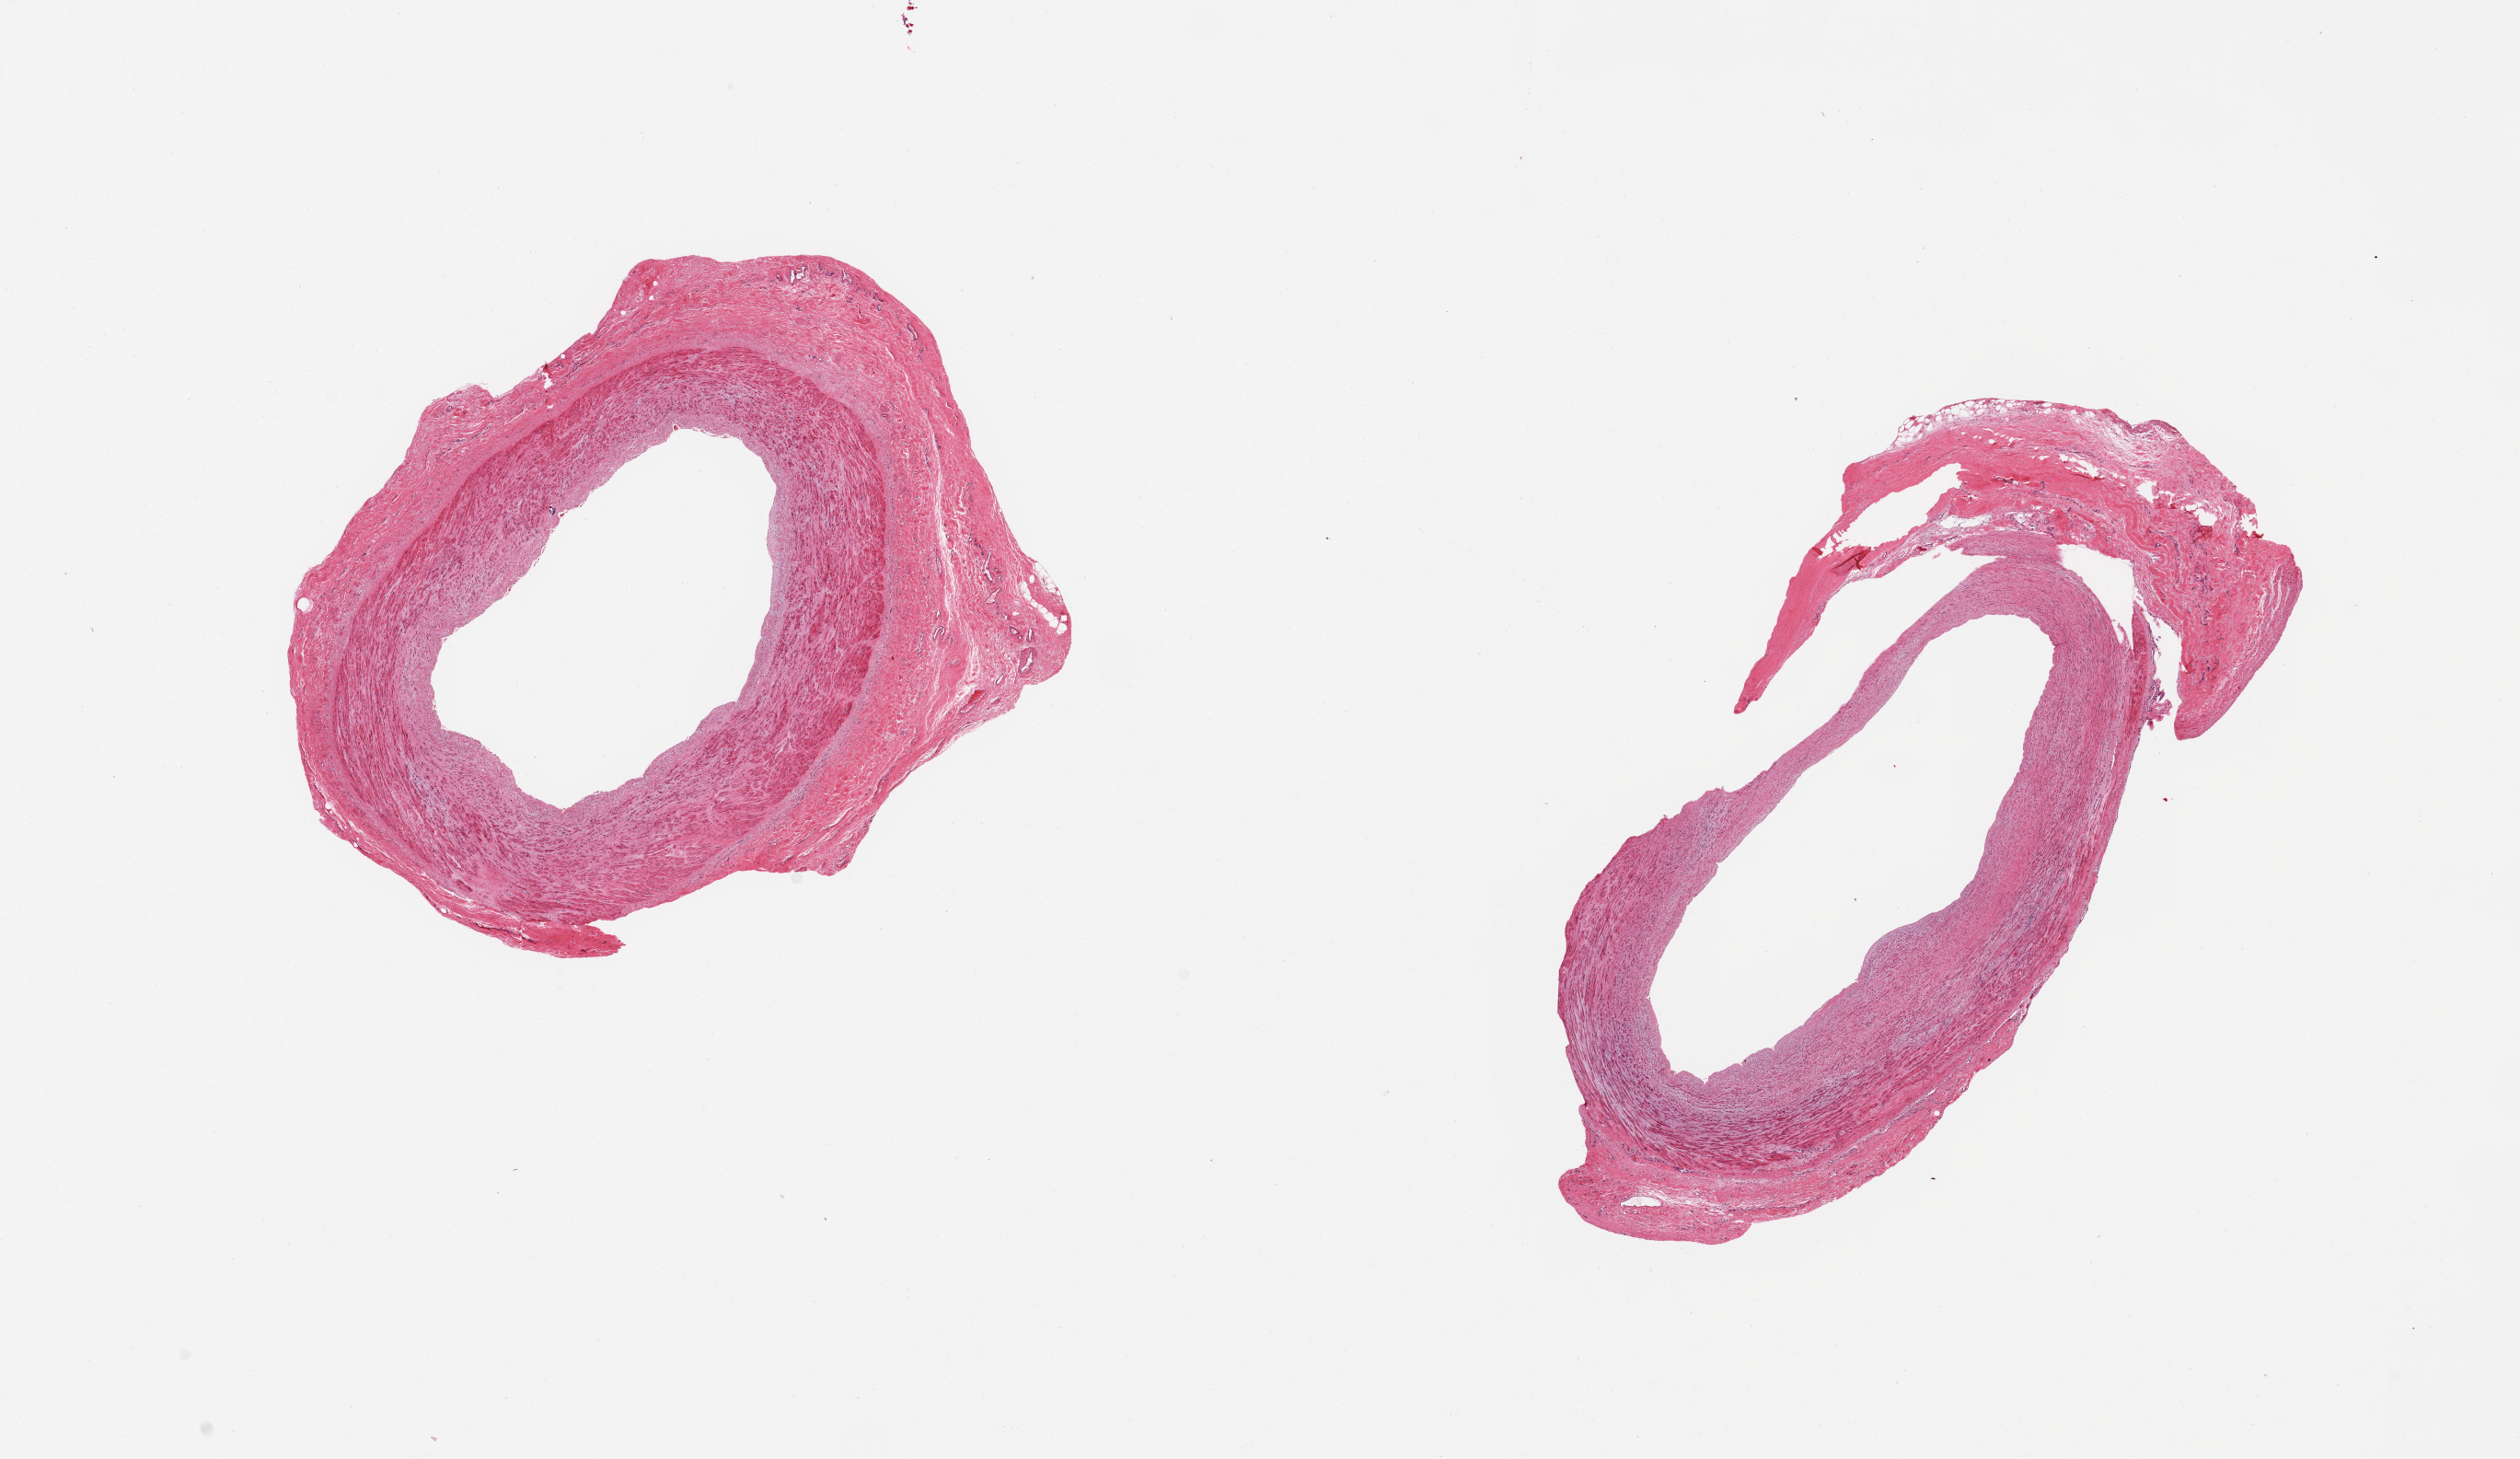
H&E whole-slide image, brightfield — low-resolution overview of the scanned area, about 21.7 x 12.5 mm (acquisition: 20x scan). PAXgene-fixed paraffin-embedded (PFPE) section. Sampled site (target tissue): tibial artery. Donor tissue sample. Donor sex: male.
Review note (as recorded): 2 pieces, minimal atherosis, rim of fibrous tissue up to ~1mm.